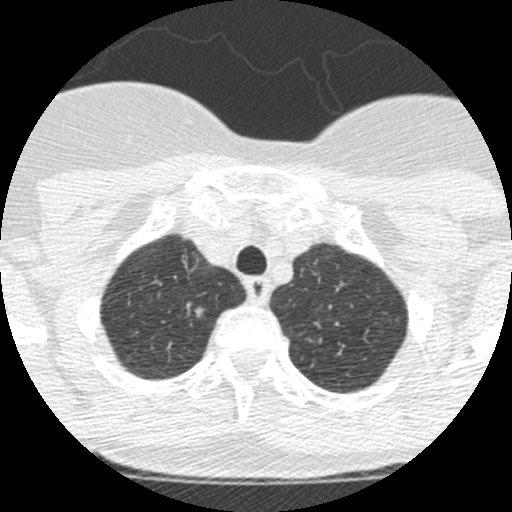
Low-dose screening chest CT, one axial slice; slice 211 of 250 in the series (ordered by position); 120 kVp; lung window (W 1500 / L -600 HU); 512 × 512 image matrix.
Outlined on this slice (expert manual segmentation):
- lesion 1 (tumor, upper lobe of right lung): bounding box (x1, y1, x2, y2) in pixels: (195, 307, 204, 317)